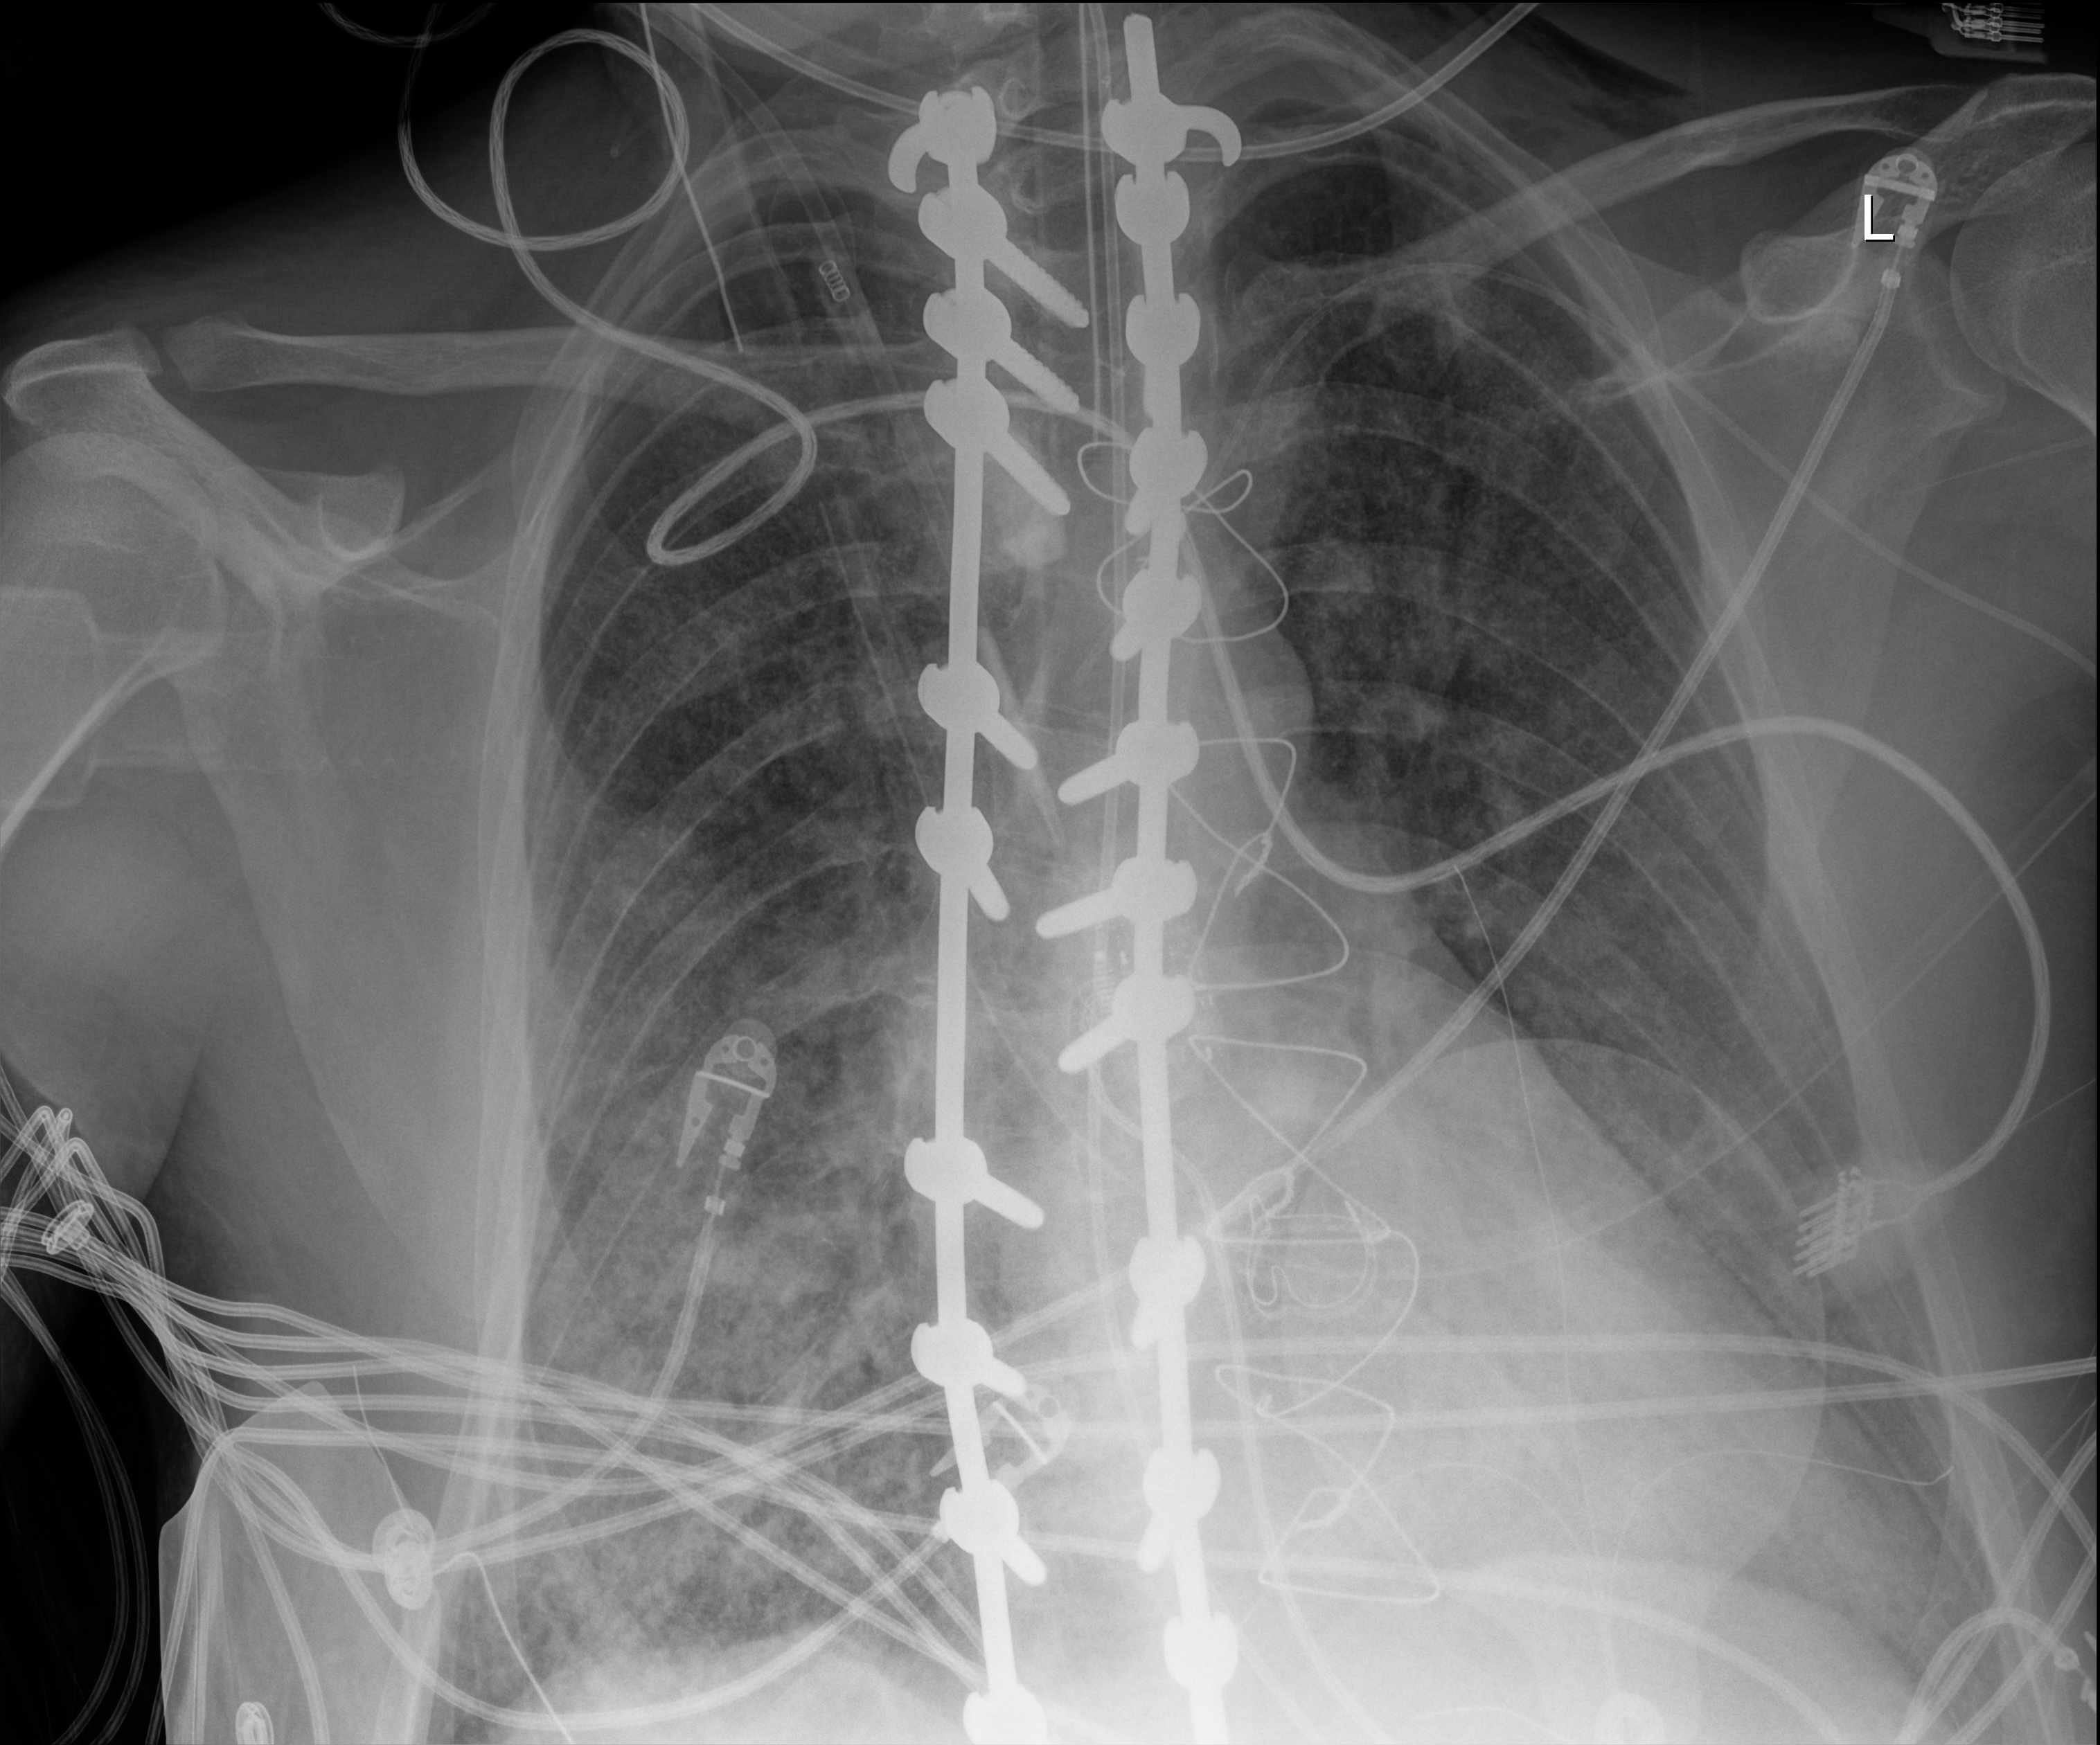
Bedside chest radiograph (digital radiography); anteroposterior (AP) projection. Adult patient hospitalised with COVID-19, age 18–59 years.
Hospital-stay facts (about this admission, not read from this image; timing relative to this image not recorded):
- COPD (admission record): no